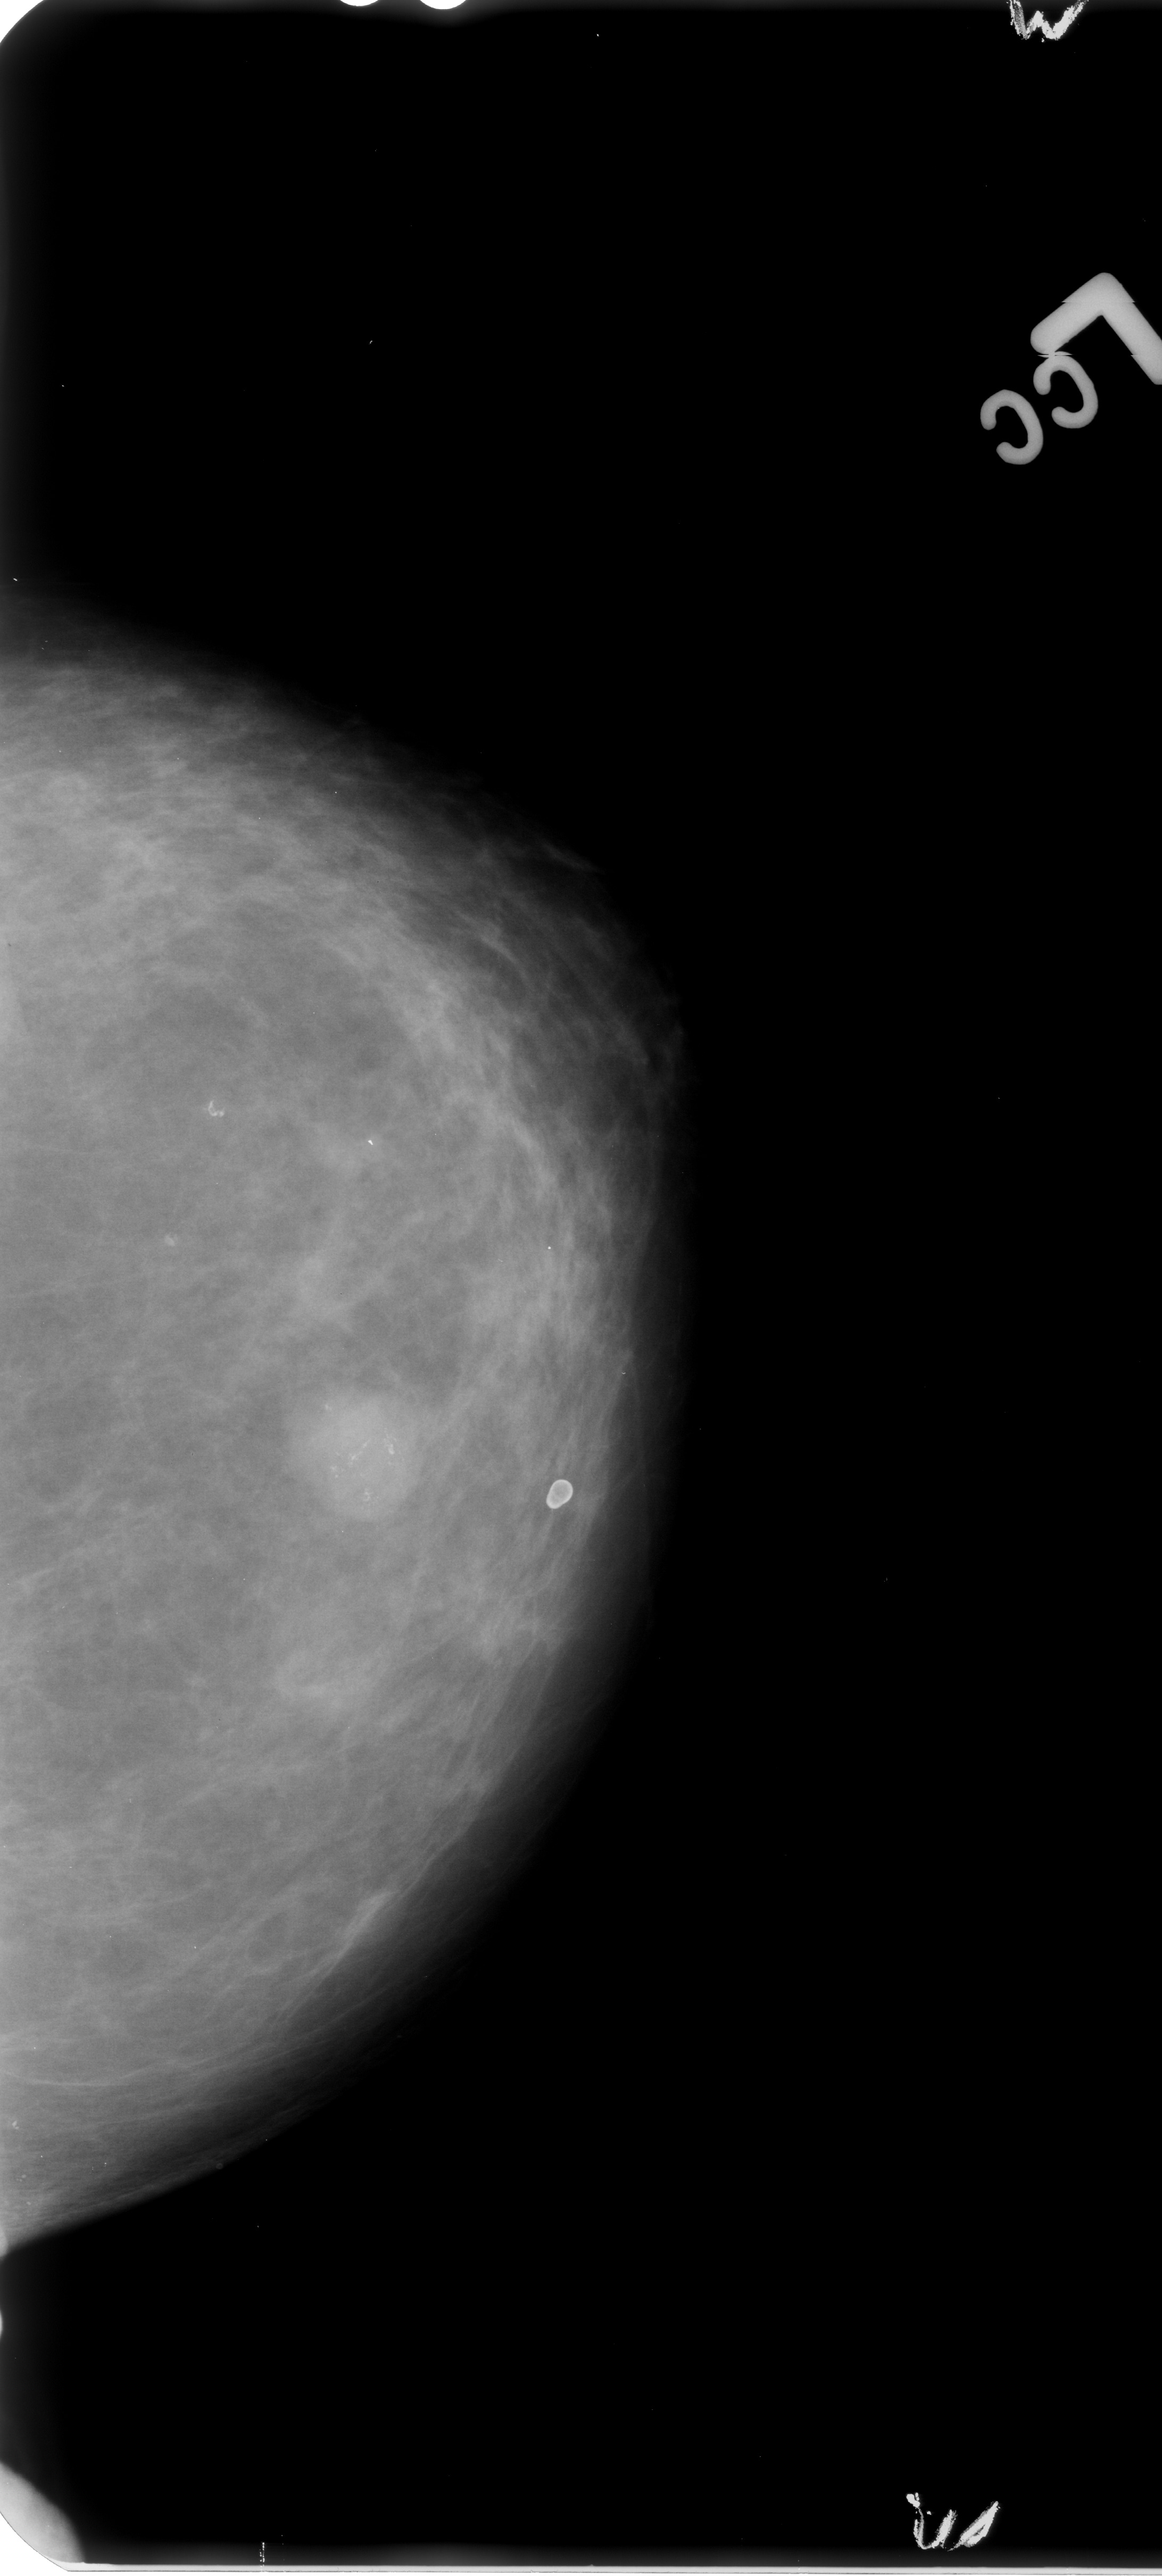
Mammogram (digitized film); left breast; craniocaudal (CC) view; breast composition: scattered fibroglandular densities (BI-RADS density category 2 of 4); 1162 × 2576 image matrix.
Expert-marked regions of interest on this film, with their recorded descriptors:
- calcifications, morphology pleomorphic, distribution clustered; BI-RADS assessment category 4; subtlety rating 5 on a 1 (subtle) to 5 (obvious) scale; pathology (as recorded): benign: bounding box [x1, y1, x2, y2] px = [280, 1379, 439, 1534]